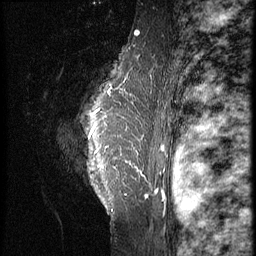
Breast MRI (dynamic contrast-enhanced), one sagittal slice; 3 images stored at this slice position (order not interpretable as contrast timing); 1.5 T; TE 4.2 ms, TR 9 ms; 2.5 mm slice thickness; 256 × 256 image matrix, field of view 180 × 180 mm. Female patient, age 39 years. From the clinical record (not read from this slice): setting: breast cancer imaged before/during neoadjuvant chemotherapy; receptor status: HER2-positive.
Outlined on this slice (semi-automatically segmented with operator editing):
- analysis volume of interest (the breast-tissue region the enhancement analysis was run in; not a lesion): bounding box (x1, y1, x2, y2) in pixels: (44, 47, 148, 239)
- tumour enhancement mask (voxels above the 140 % enhancement threshold inside the analysis volume of interest): (88, 127, 146, 196)